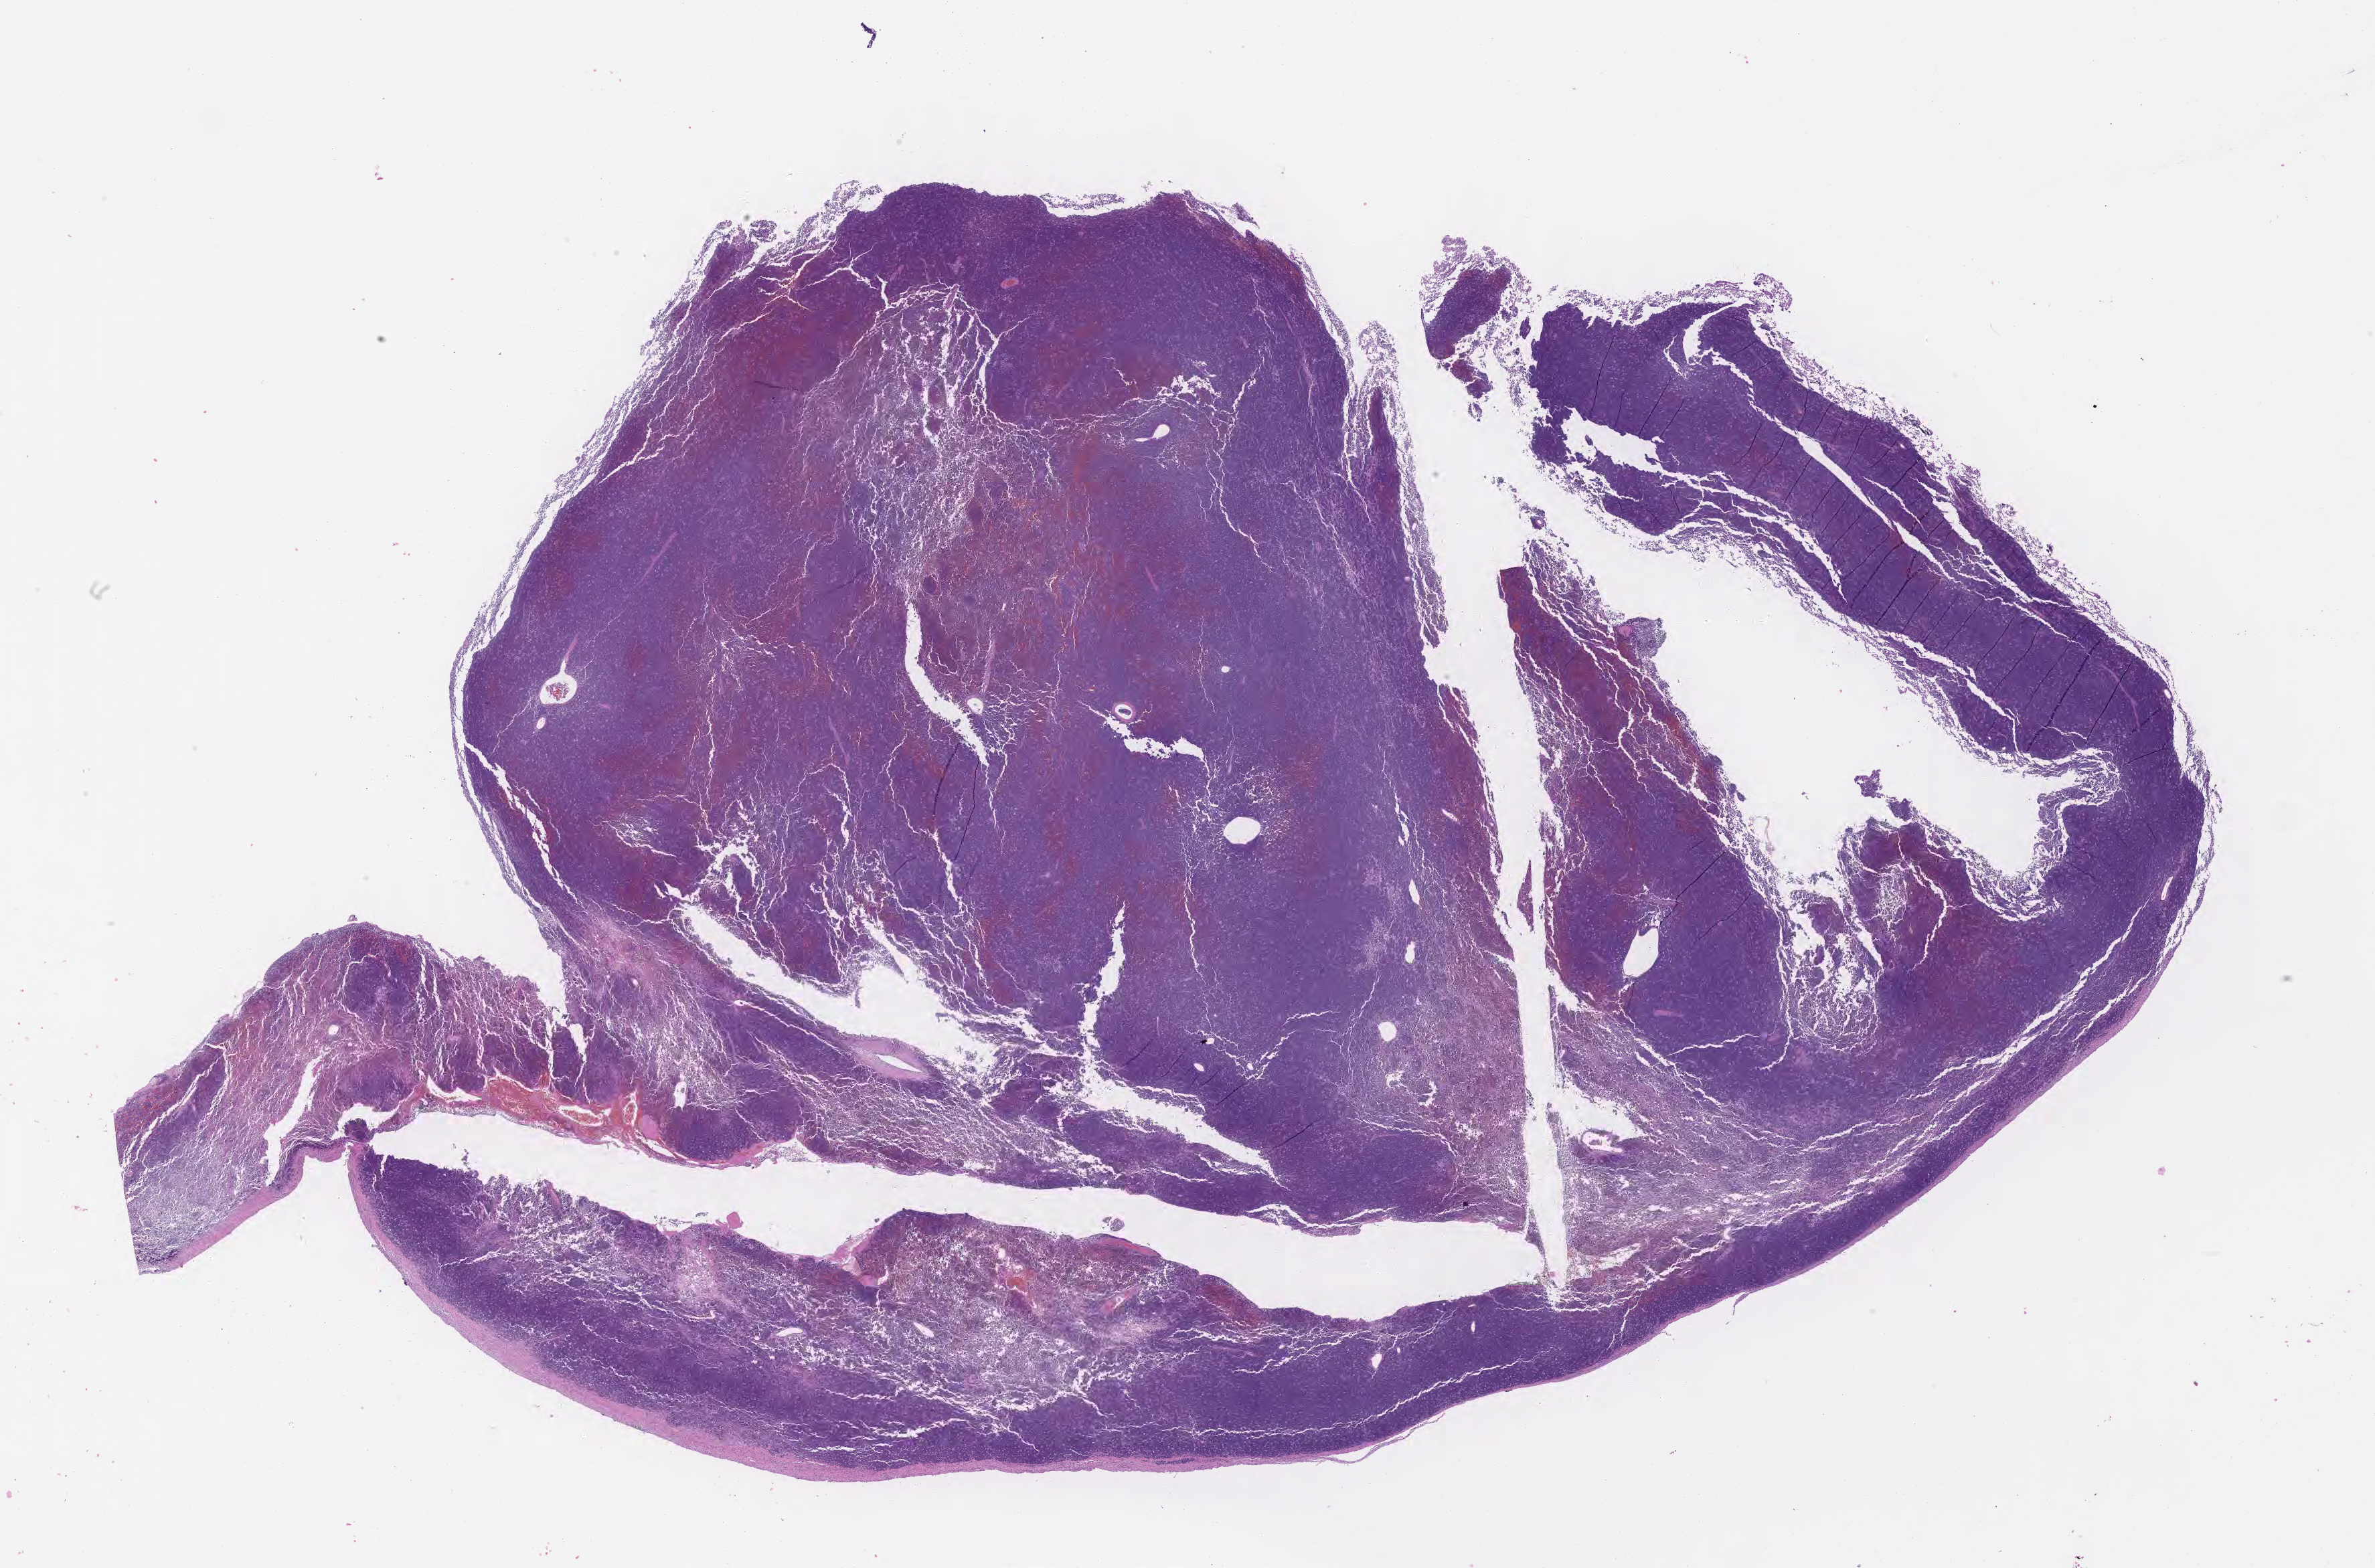
Hematoxylin and eosin (H&E) whole-slide image, low-resolution overview of the scanned area, about 28.7 x 18.9 mm; tumor tissue. Patient: female, age at initial diagnosis 3 years.
Histologic diagnosis: Burkitt lymphoma, NOS.